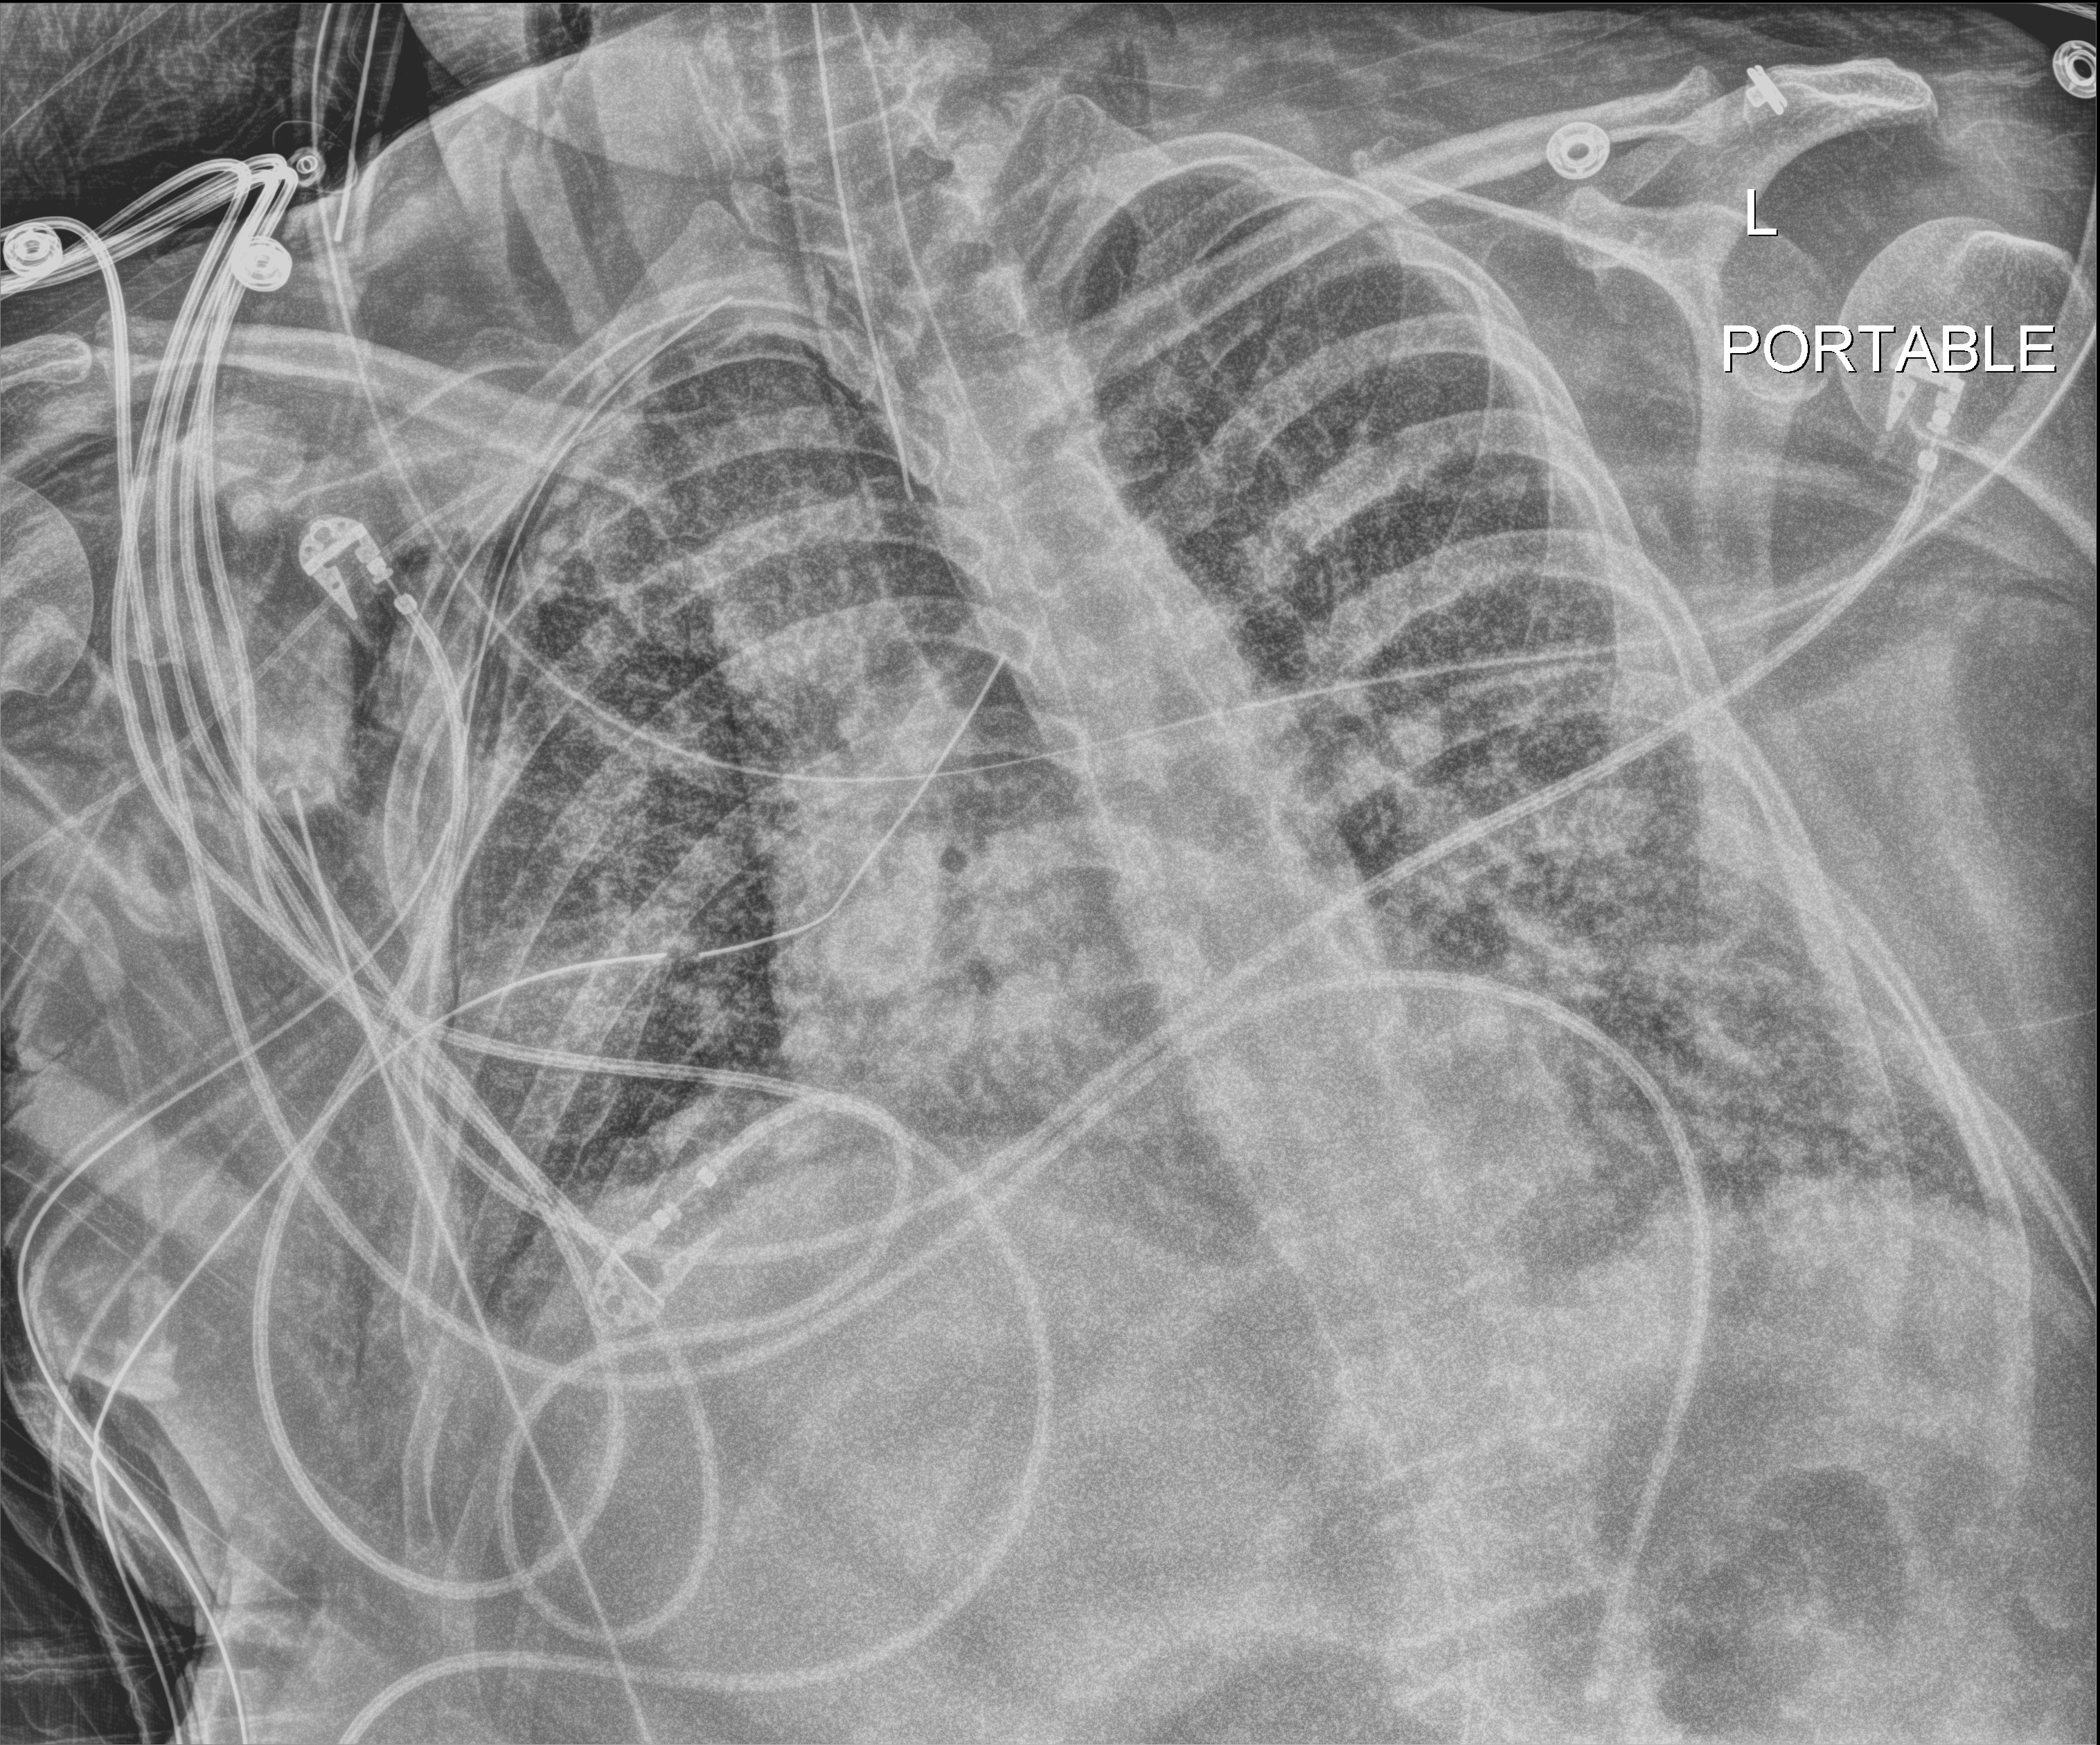
Bedside chest radiograph (digital radiography); anteroposterior (AP) projection. Adult patient hospitalised with COVID-19, age 18–59 years.
From the hospital-stay record, not from the radiograph (when in the stay this image was taken is not recorded):
- admitted to intensive care during this hospital stay: yes
- COPD (admission record): no